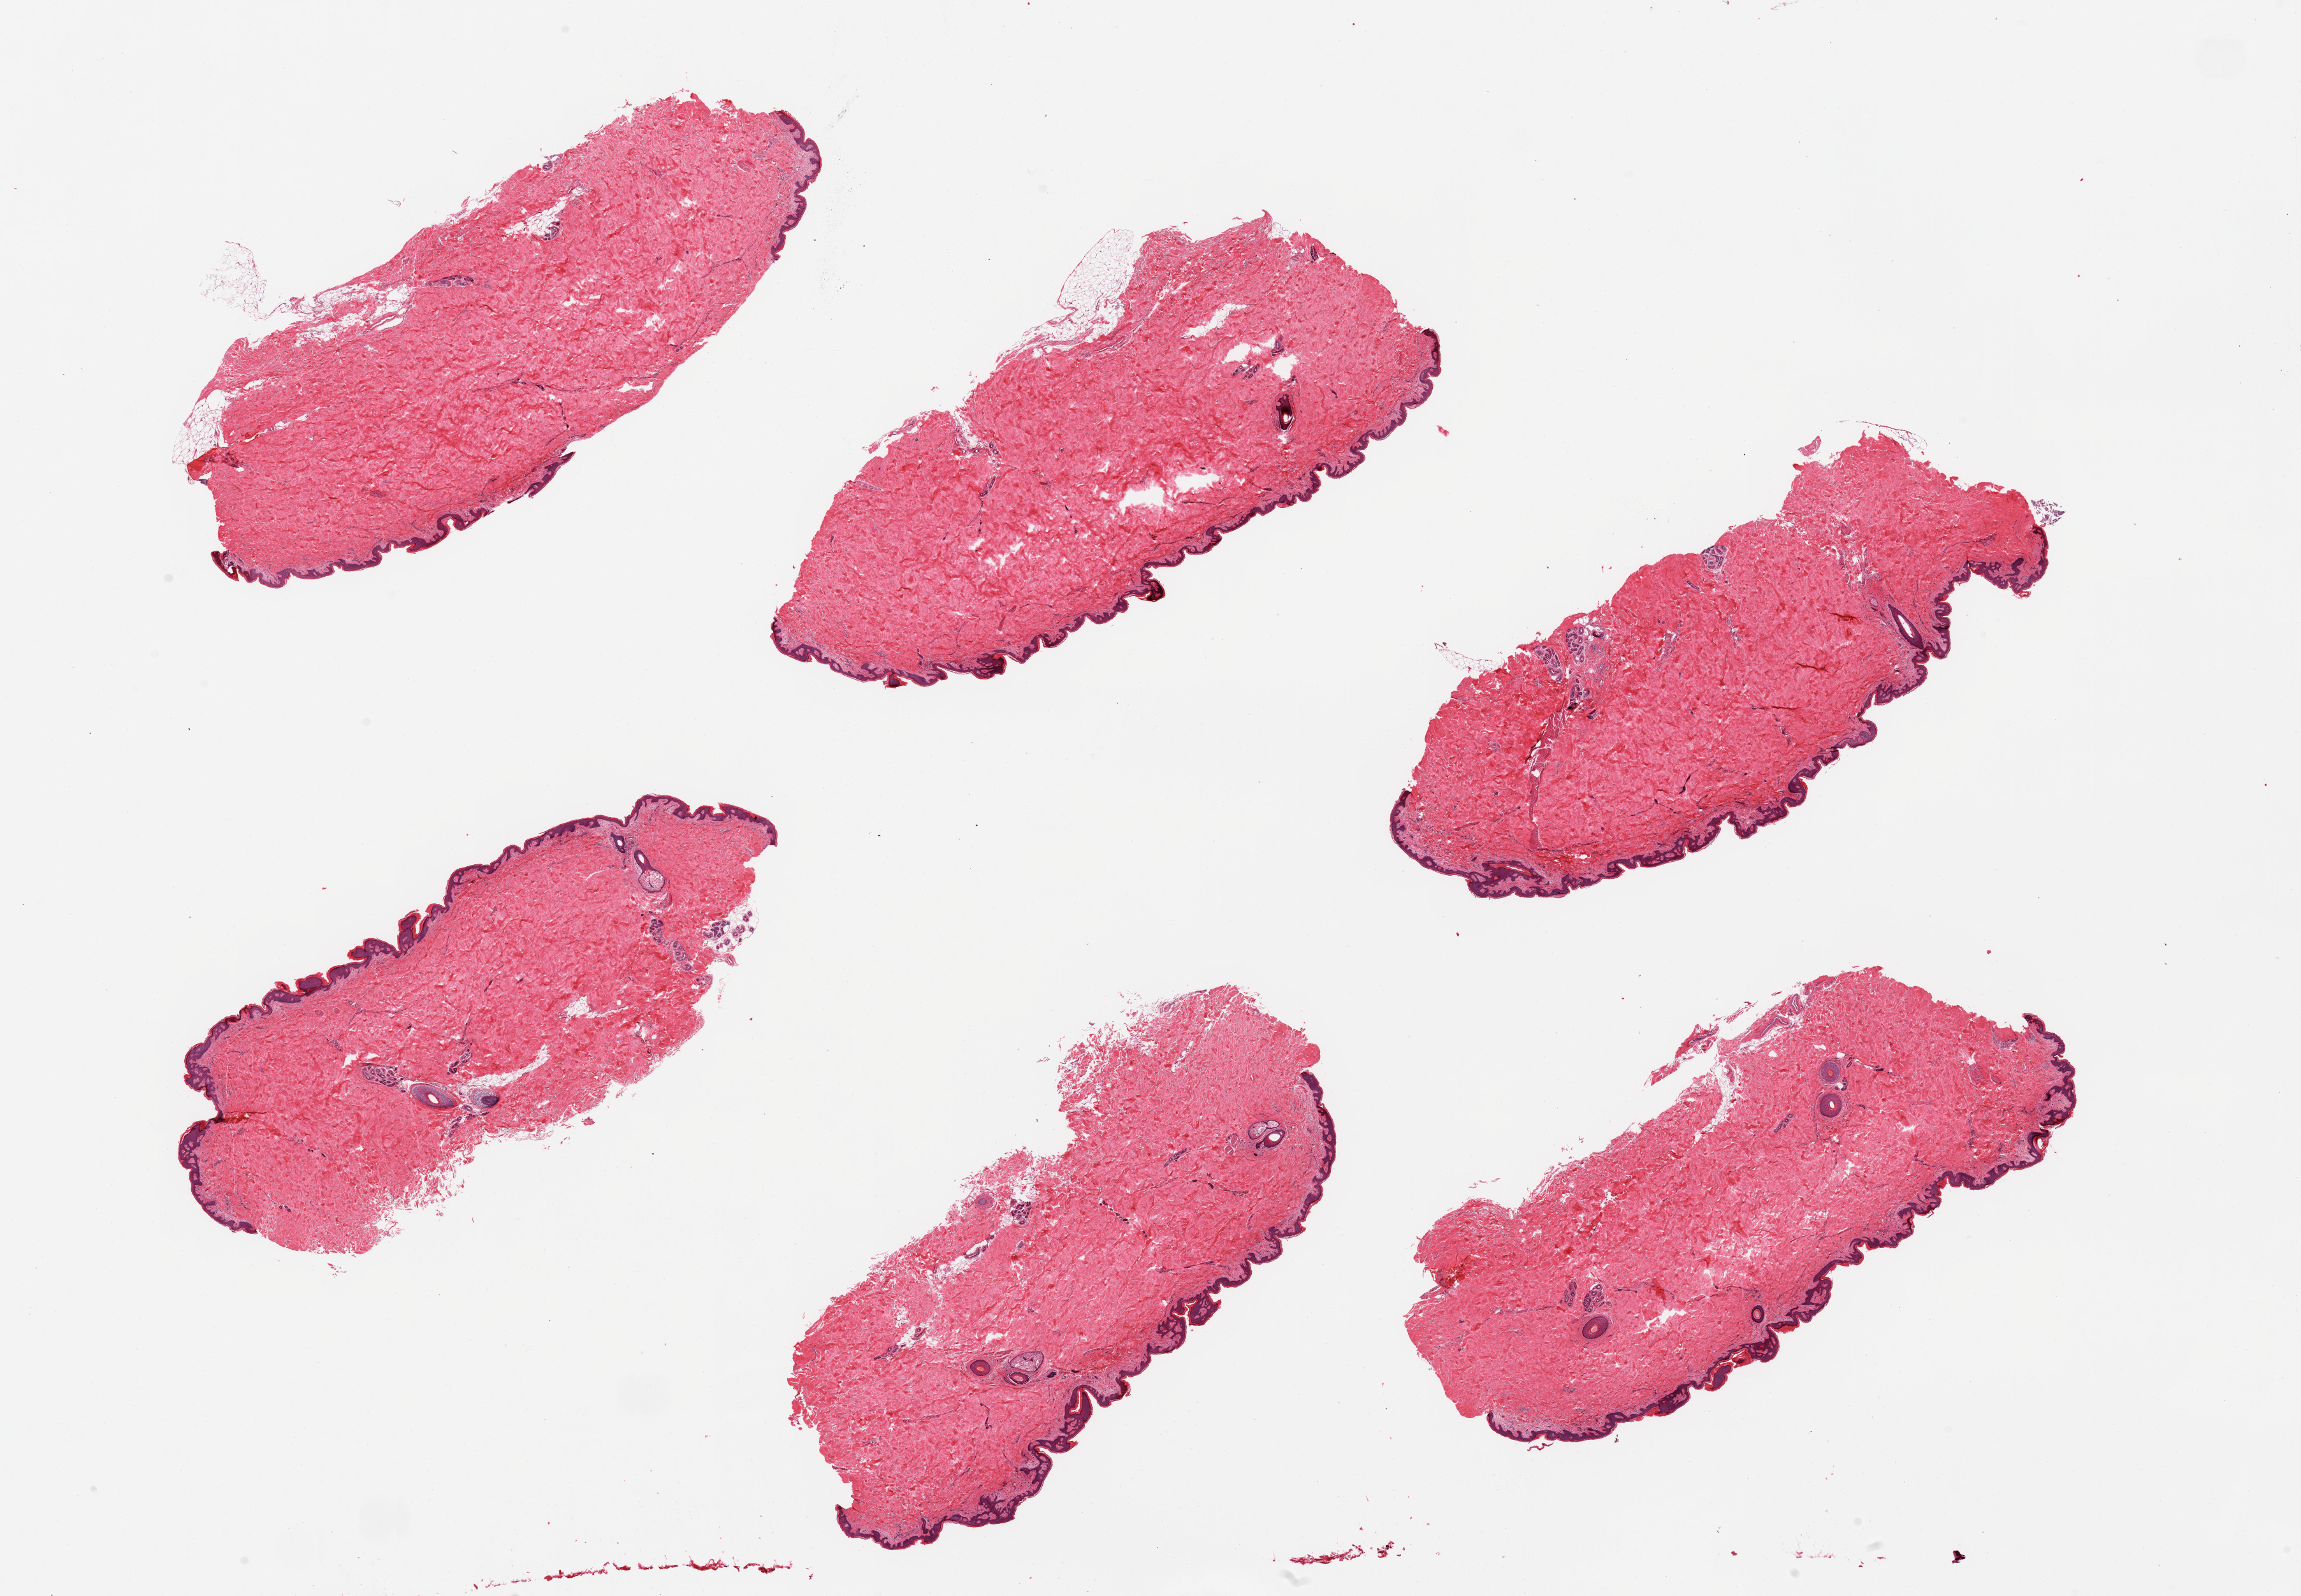
H&E whole-slide image — low-resolution overview of the scanned area, about 28.5 x 19.8 mm (from a 20x scan), PAXgene-fixed, paraffin-embedded tissue, sampled site (target tissue): skin of suprapubic region, donor tissue sample. Male donor.
Reviewer comment on this tissue sample: 6 pieces; well trimmed; several hair follicles; <10% intradermal fat.